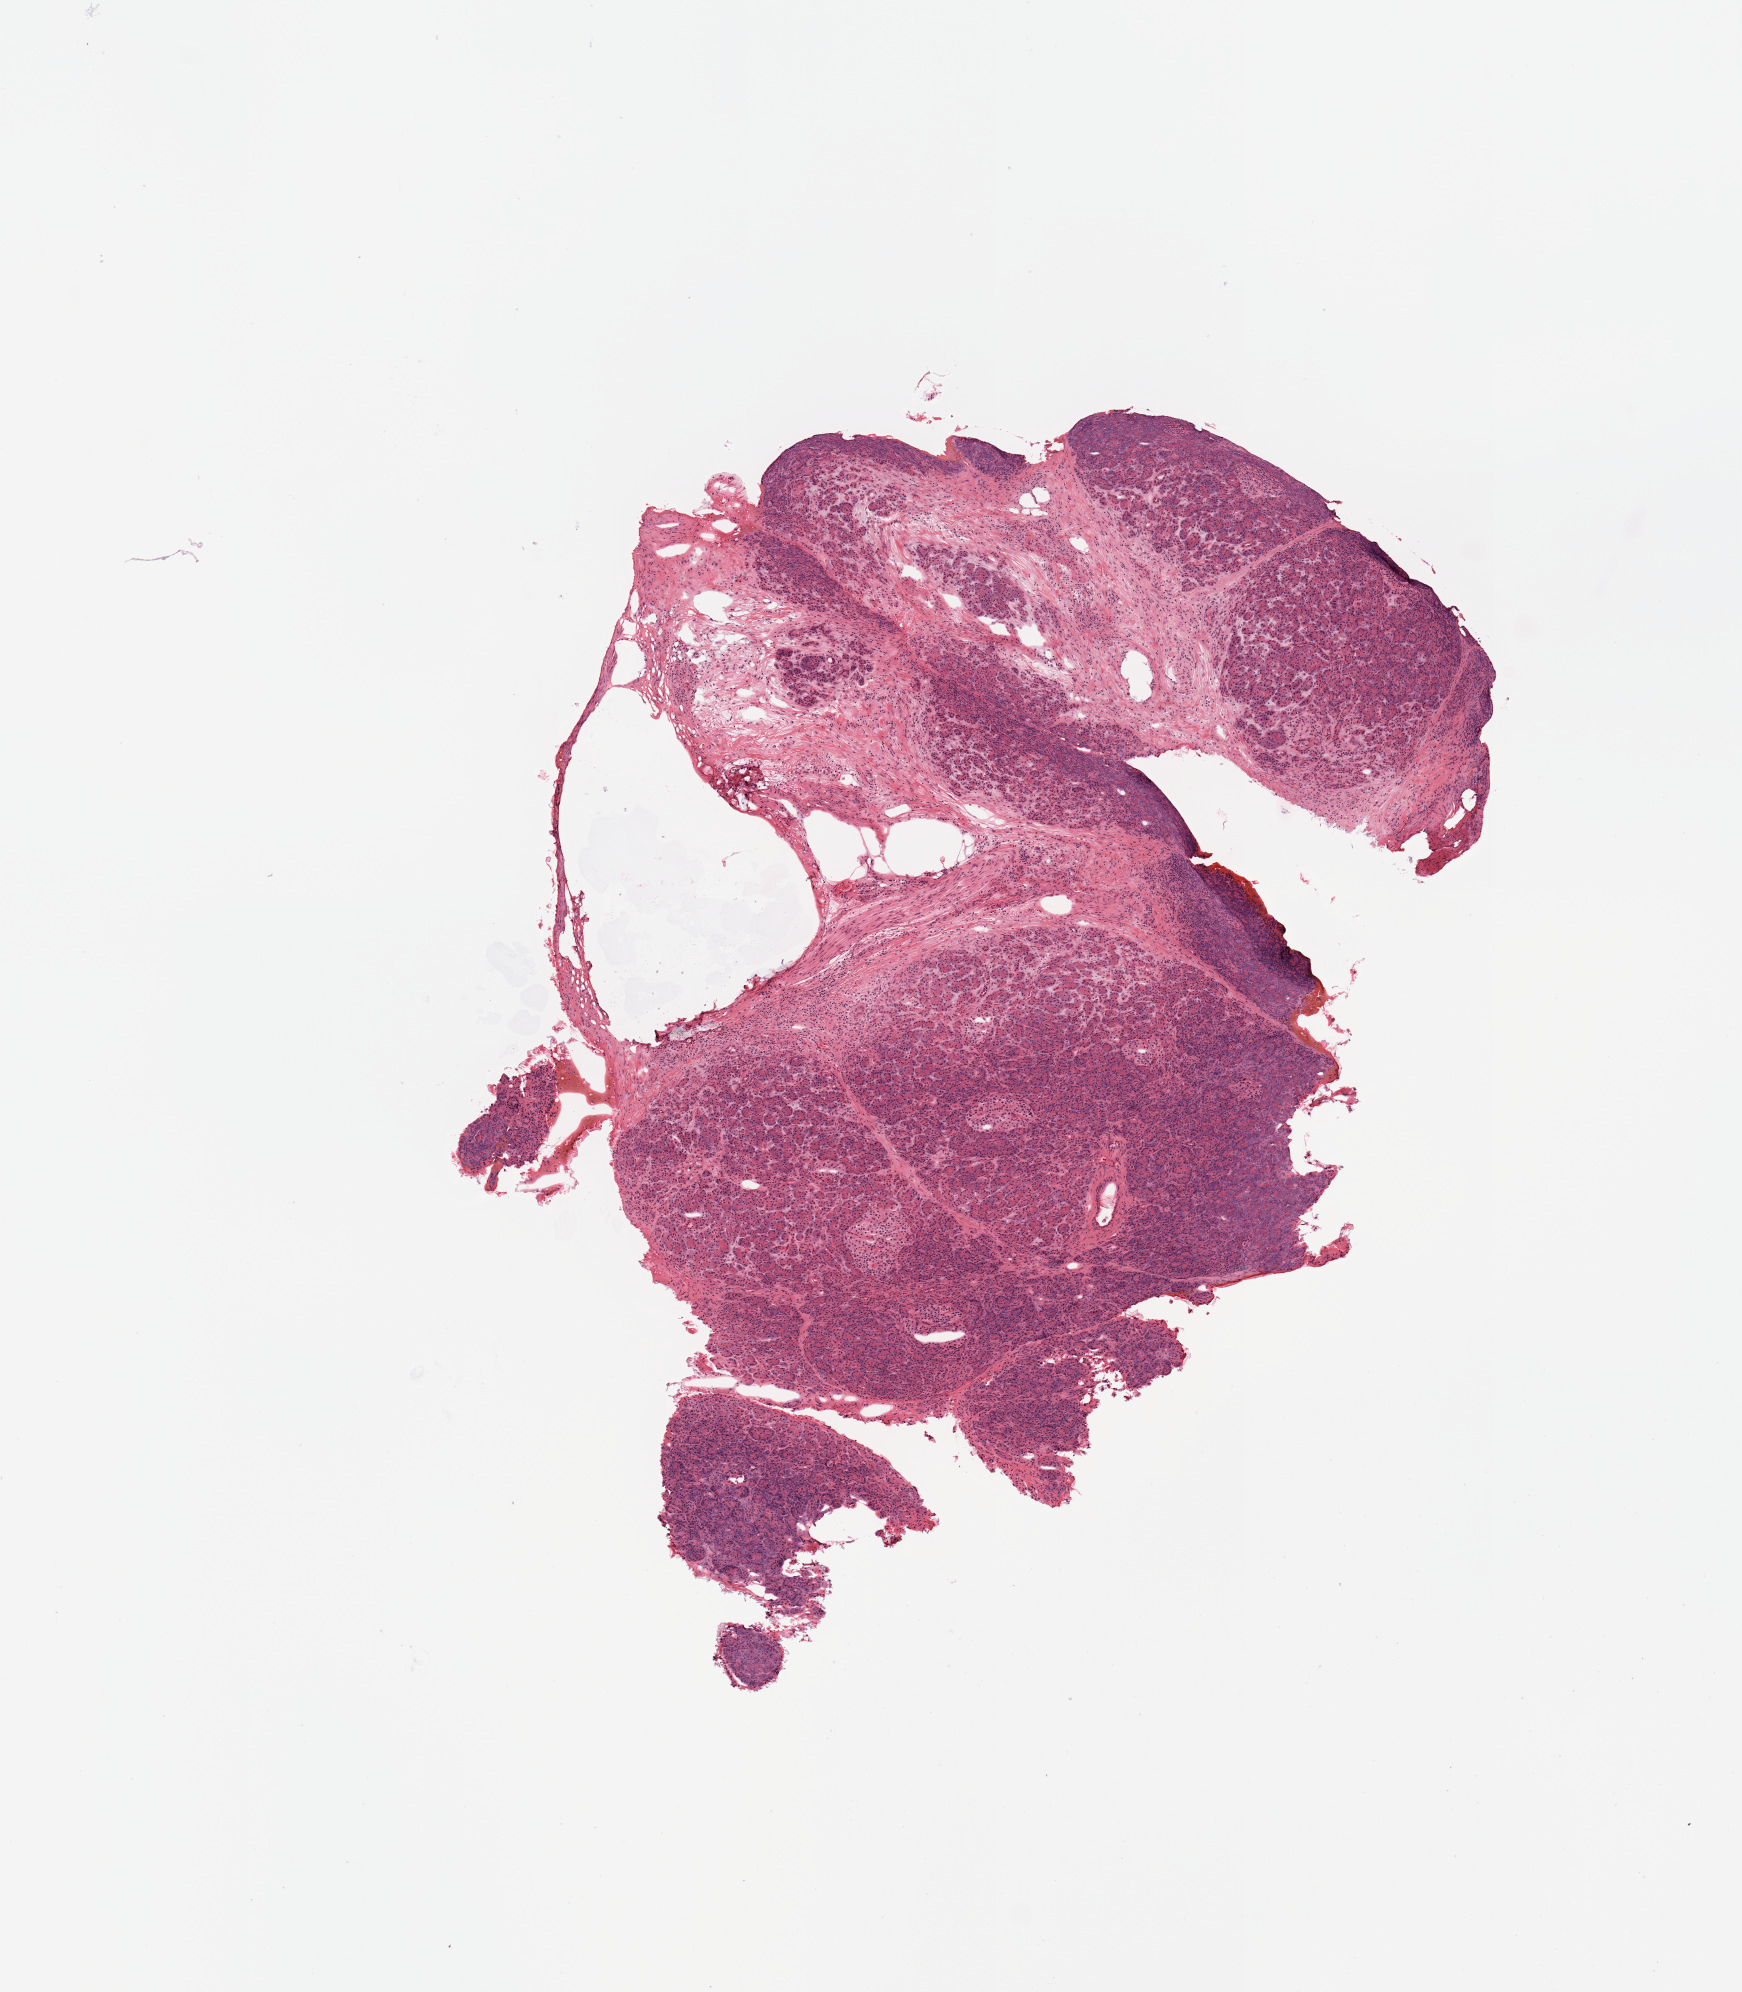
Digitized H&E tissue section (whole slide), a low-resolution overview of the entire scanned area, about 6.9 x 7.9 mm. Normal (non-tumour) tissue sample, pancreas. 62-year-old male patient.
- this section: normal (non-tumour) tissue from the same patient
- patient diagnosis: Infiltrating duct carcinoma, NOS